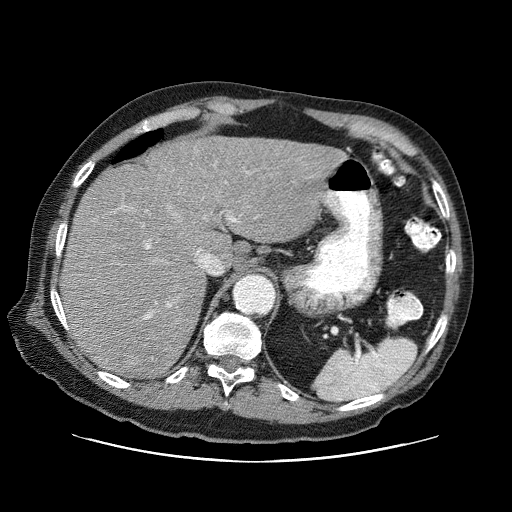
Contrast-enhanced abdominal CT (liver protocol), one axial slice. Position 53 of 87 along the scan axis. Reconstruction kernel STANDARD. 120 kVp. One of 3 acquisitions stored at this slice position. Soft-tissue window (W 400 / L 40 HU). 2.5 mm slice thickness. 512 × 512 image matrix. From the clinical record (not read from this slice): diagnosis: hepatocellular carcinoma (patient treated with transarterial chemoembolisation; whether this scan precedes or follows treatment is not stated here); TNM stage (as recorded): Stage-IIIA; Child-Pugh class: A; tumour differentiation: well differentiated; tumour size: 6 cm.
Outlined on this slice (semi-automatic segmentation, software-assisted and operator-edited):
- abdominal aorta: bounding box [x1, y1, x2, y2] px = [236, 274, 274, 314]
- liver parenchyma outside the tumour (the mass and vessels are separate outlines, so this box may not span the whole liver): [60, 136, 346, 376]
- liver vessels: [117, 172, 248, 320]